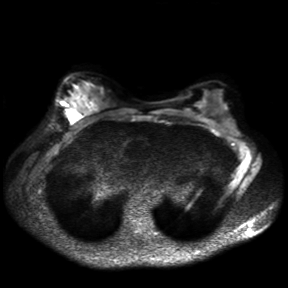
Breast MRI, one axial slice; position 21 of 30 along the scan axis; diffusion-weighted series; image 2 of 4 stored at this slice position (different b-values; order by instance number); 3 T; 4 mm slice thickness; 288 × 288 image matrix, field of view 360 × 360 mm. Female patient.
Outlined on this slice (expert manual segmentation):
- tumour on diffusion-weighted imaging: bounding box (x1, y1, x2, y2) in pixels: (68, 110, 79, 120)